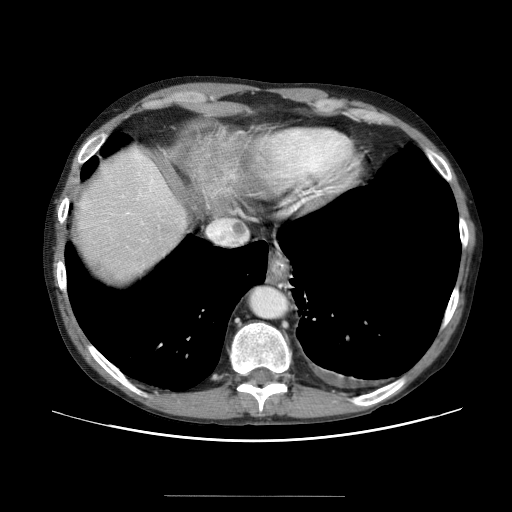
Contrast-enhanced abdominal CT (liver protocol), one axial slice; position 56 of 69 along the scan axis; reconstruction kernel STANDARD; soft-tissue window (W 400 / L 40 HU); 512 × 512 image matrix, field of view 380 × 380 mm. Case-level facts recorded for this patient, not image findings: diagnosis: hepatocellular carcinoma (patient treated with transarterial chemoembolisation; whether this scan precedes or follows treatment is not stated here); TNM stage (as recorded): Stage-IVB; Child-Pugh class: B; tumour differentiation: poorly differentiated; tumour nodularity: multinodular.
Outlined on this slice (semi-automatic segmentation, software-assisted and operator-edited):
- liver parenchyma outside the tumour (the mass and vessels are separate outlines, so this box may not span the whole liver): bounding box <70,124,268,308> (left, top, right, bottom; pixels)
- liver vessels: <126,198,156,226>